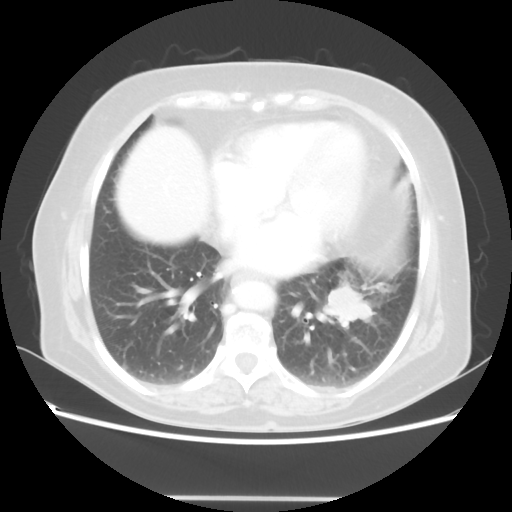
Chest CT, one axial slice; slice 22 of 56 in the series (ordered by position); 100 kVp; lung window (W 1500 / L -600 HU); 5 mm slice thickness; 512 × 512 image matrix, field of view 360 × 360 mm. Patient: female, 73 years. From the clinical record (not read from this slice): clinical TNM (as recorded): T1c N0 M0.
Outlined on this slice (bounding box drawn by a radiologist):
- lung tumour (recorded histology: adenocarcinoma): bounding box [x1, y1, x2, y2] px = [326, 282, 376, 332]